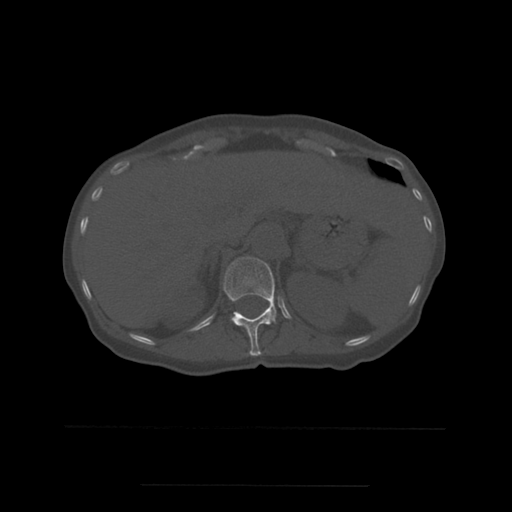
CT including the spine, one axial slice. Position 256 of 544 along the scan axis. Bone window (W 1800 / L 400 HU). 1.25 mm slice thickness. 512 × 512 image matrix, field of view 350 × 350 mm. Patient age 58 years. Case-level facts recorded for this patient, not image findings: primary cancer: lung.
Outlined on this slice (semi-automatic segmentation, software-assisted and operator-edited):
- T12 vertebra: bounding box [x1, y1, x2, y2] px = [224, 257, 277, 356]